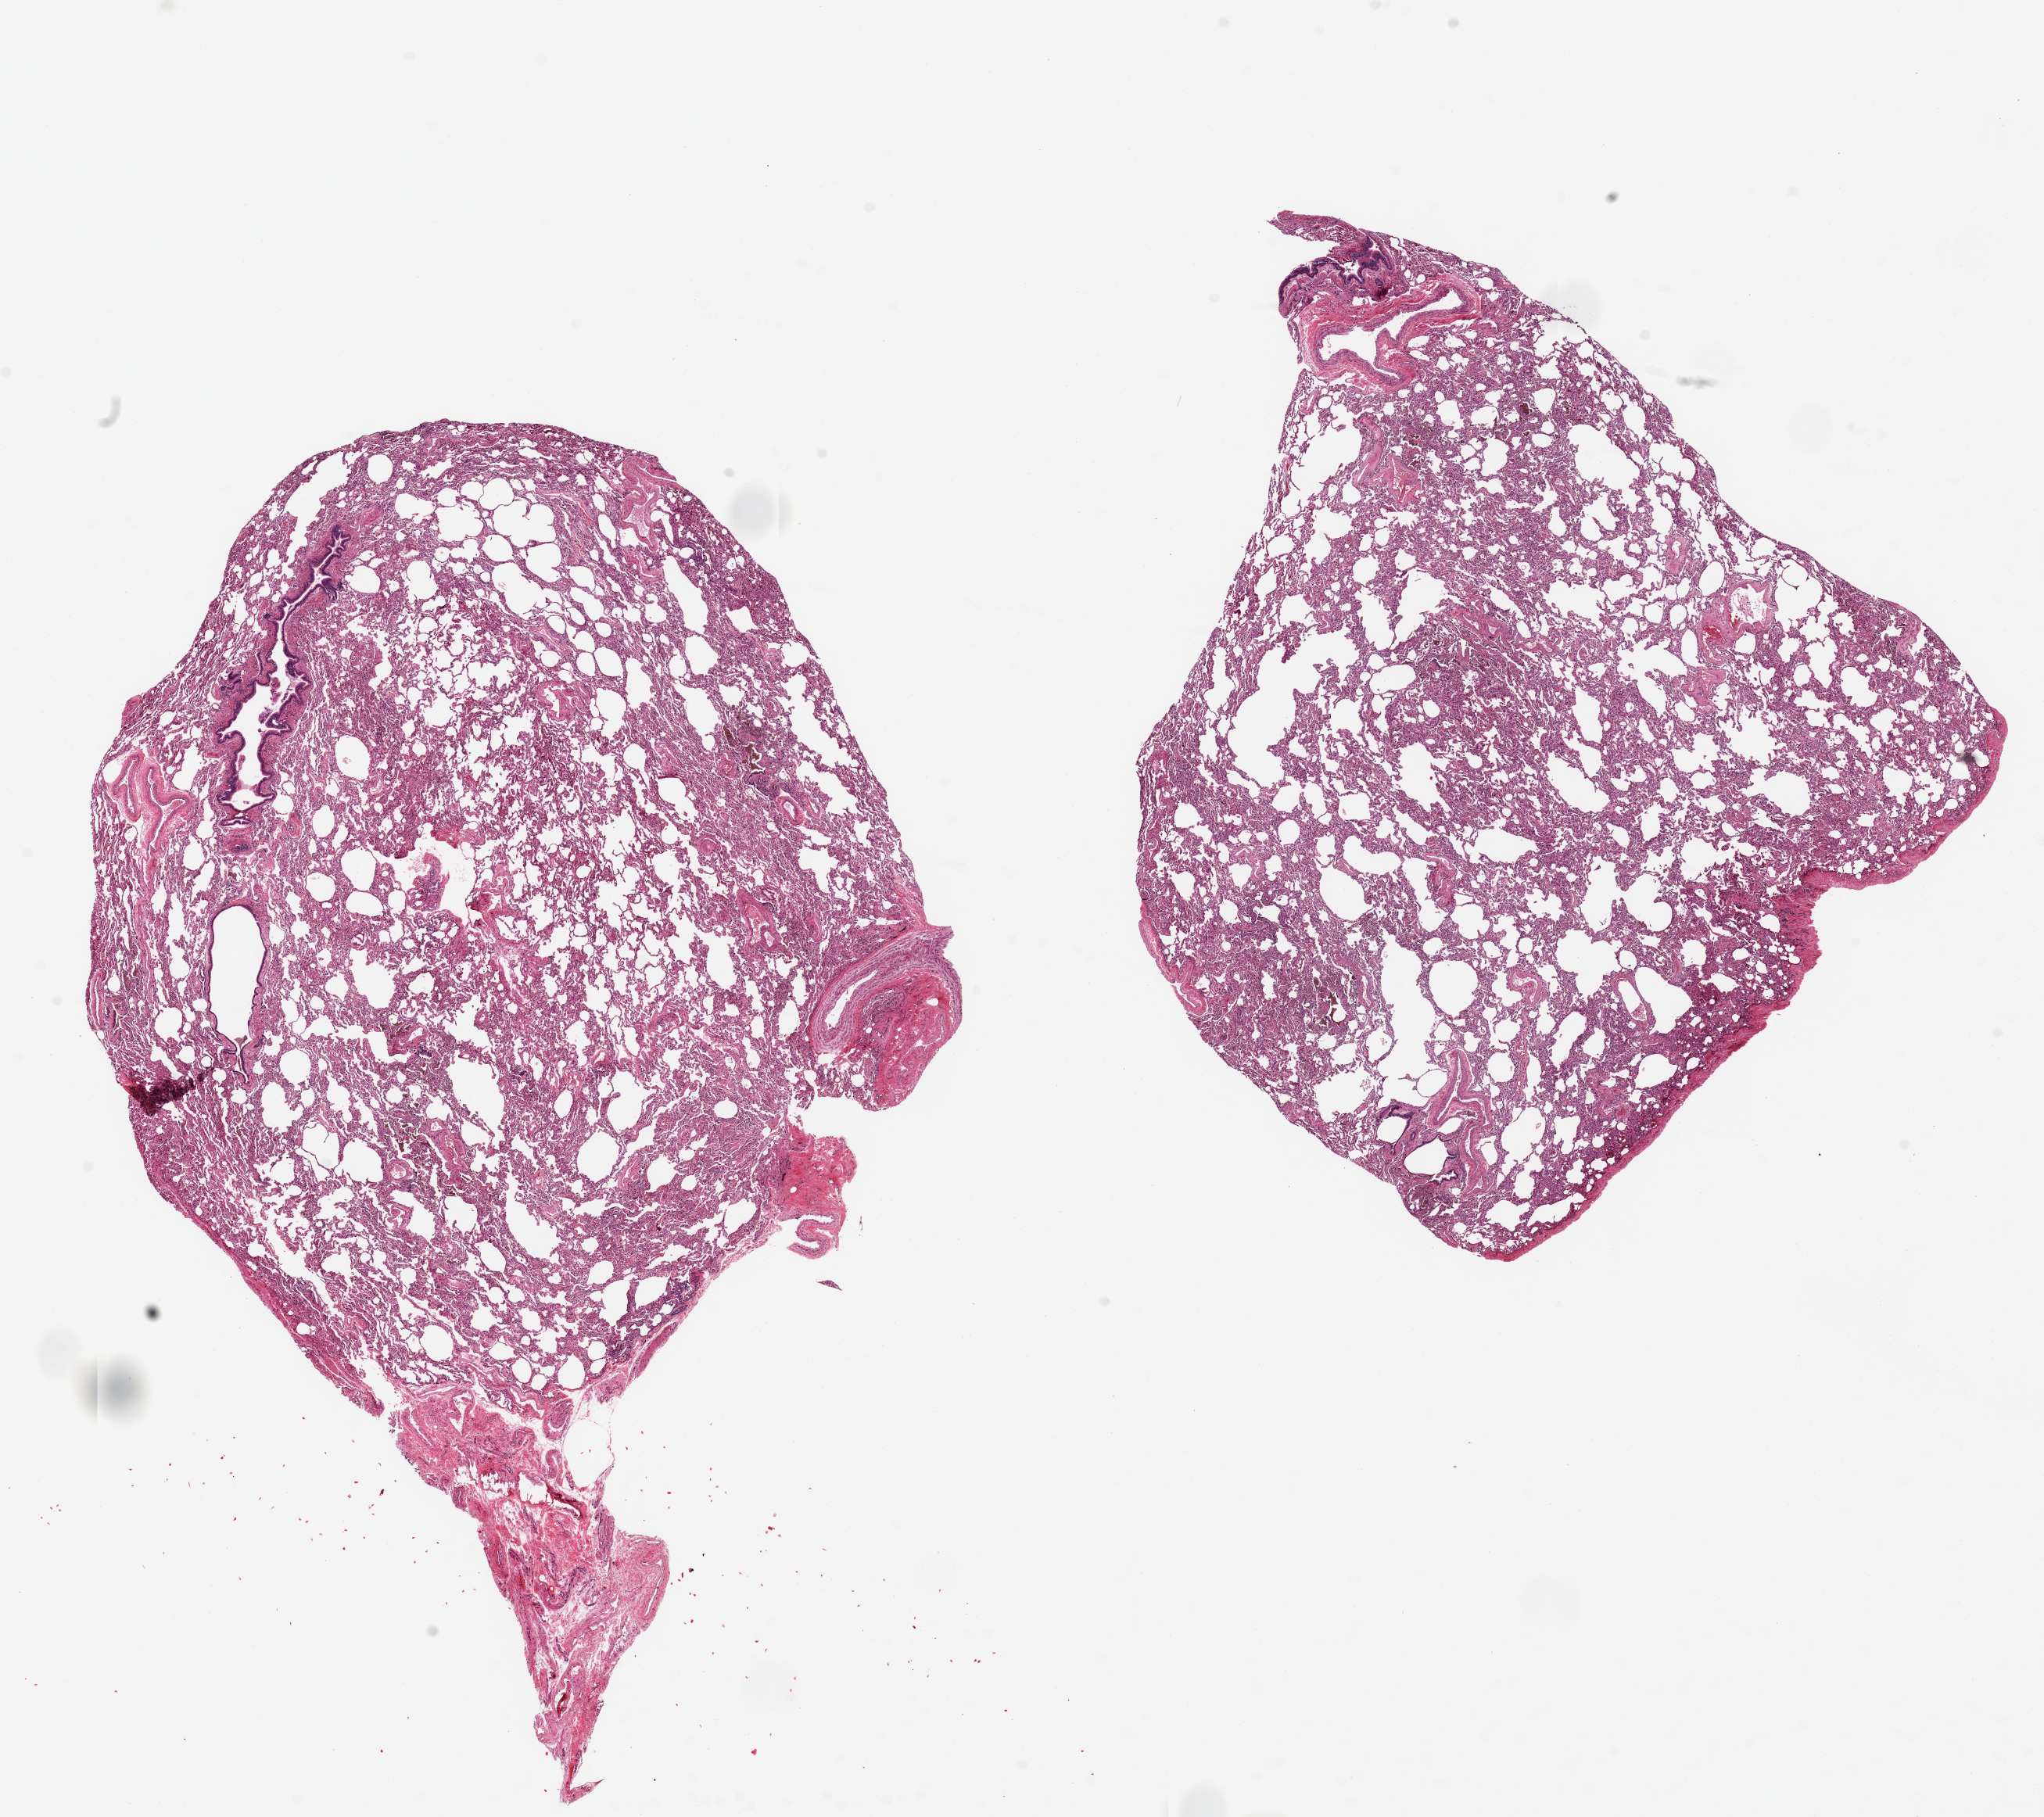
Hematoxylin and eosin (H&E) whole-slide image — shown as a low-resolution overview of the whole scanned area (about 20.7 x 18.4 mm, acquisition: 20x scan). PAXgene-fixed paraffin-embedded (PFPE) section. Target tissue: lung. Tissue donor sample. Female donor.
Pathologist's review note for this sample: 2 pieces, 9x7 & 9x7.5mm; no inflammation.